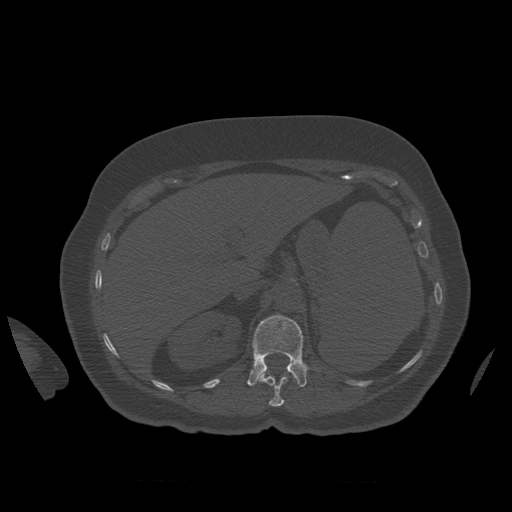
CT including the spine, one axial slice. Position 286 of 399 along the scan axis. Reconstruction kernel STANDARD. 120 kVp. Bone window (W 1800 / L 400 HU). 1.25 mm slice thickness. 512 × 512 image matrix, field of view 404 × 404 mm. Patient age 81 years. From the clinical record (not read from this slice): primary cancer: renal.
Annotated regions visible in this slice (semi-automatic segmentation, software-assisted and operator-edited):
- L1 vertebra: bounding box [x1, y1, x2, y2] px = [247, 315, 309, 387]
- T12 vertebra: [259, 372, 296, 407]